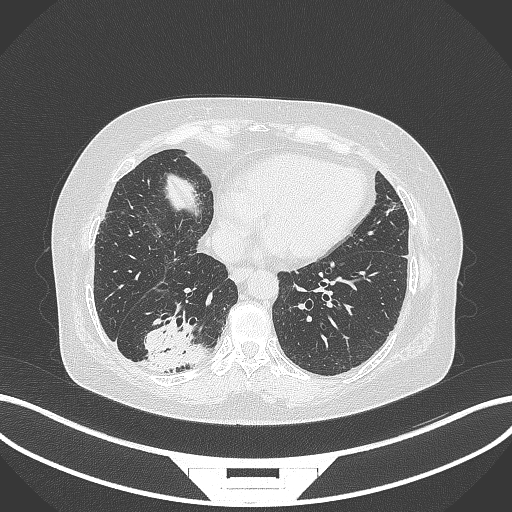
Chest CT, one axial slice. 120 kVp. Lung window (W 1500 / L -600 HU). 1 mm slice thickness. 512 × 512 image matrix, field of view 400 × 400 mm. Female patient, age 65 years. Case-level facts recorded for this patient, not image findings: clinical TNM (as recorded): T2b N1 M0.
Annotated regions visible in this slice (bounding box drawn by a radiologist):
- lung tumour (recorded histology: adenocarcinoma): bounding box [x1, y1, x2, y2] px = [140, 315, 208, 373]